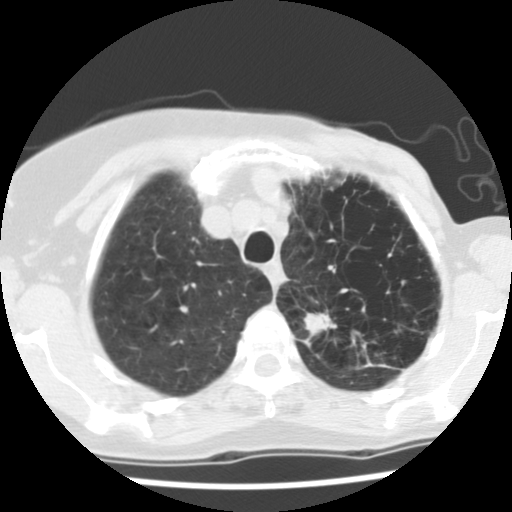
Low-dose screening chest CT, one axial slice. Slice 104 of 128 in the series (ordered by position). Reconstruction kernel STANDARD. 140 kVp. Lung window (W 1500 / L -600 HU). 2.5 mm slice thickness. 512 × 512 image matrix.
Annotated regions visible in this slice (expert manual segmentation):
- lesion 1 (tumor, upper lobe of left lung): bounding box [x1, y1, x2, y2] px = [304, 313, 336, 338]